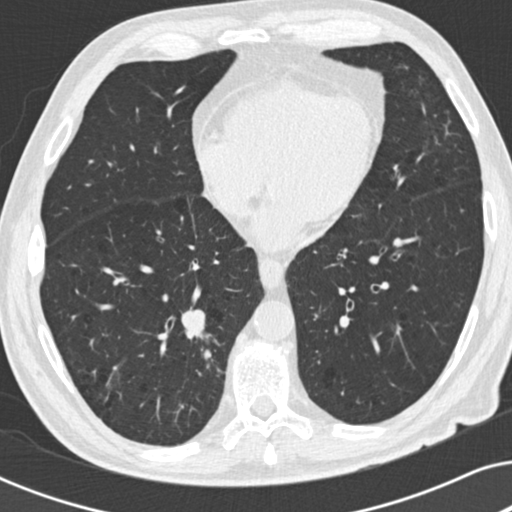
Chest CT (low-dose screening protocol), one axial image, baseline annual screen, lung window (W 1500 / L -600 HU), 2 mm slice thickness, standard (soft-tissue) reconstruction kernel (B30f). Male participant, aged 73 years at enrolment. Current smoker at enrolment.
Lesion marked by an expert reader, bounding box <162,299,224,361> (left, top, right, bottom; pixels). The screening reader recorded 2 non-calcified nodules or masses ≥4 mm on this exam (right lower lobe, right upper lobe); which of them this box marks is not recorded. Later outcome: lung cancer diagnosed 63 days after this screen — carcinoid tumor, NOS, right lower lobe, carcinoid, stage not assessed, 12 mm at pathology.